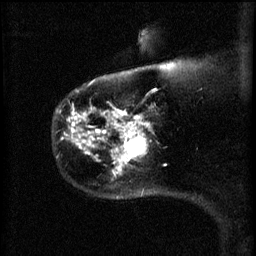
Breast MRI (dynamic contrast-enhanced), one sagittal slice. Slice 51 of 60 in the series (ordered by position). 3 images stored at this slice position (order not interpretable as contrast timing). 1.5 T. TE 4.2 ms, TR 11 ms. 2 mm slice thickness. 256 × 256 image matrix. Patient: female, 44 years.
Outlined on this slice (semi-automatic segmentation, software-assisted and operator-edited):
- analysis volume of interest (the breast-tissue region the enhancement analysis was run in; not a lesion): bounding box [x1, y1, x2, y2] px = [110, 124, 151, 175]
- tumour enhancement mask (voxels above the 70 % enhancement threshold inside the analysis volume of interest): [116, 124, 151, 175]